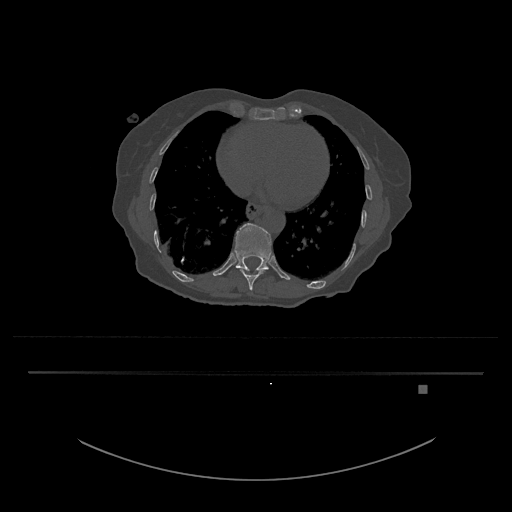
CT including the spine, one axial slice; position 688 of 797 along the scan axis; reconstruction kernel Br40s/3; bone window (W 1800 / L 400 HU); 512 × 512 image matrix, field of view 500 × 500 mm. Patient: female, 57 years. Case-level facts recorded for this patient, not image findings: primary cancer: cervical.
Outlined on this slice (semi-automatically segmented with operator editing):
- T10 vertebra: box from (x=239, y=268) to (x=267, y=291) px
- T11 vertebra: (x=234, y=223)–(x=271, y=271)